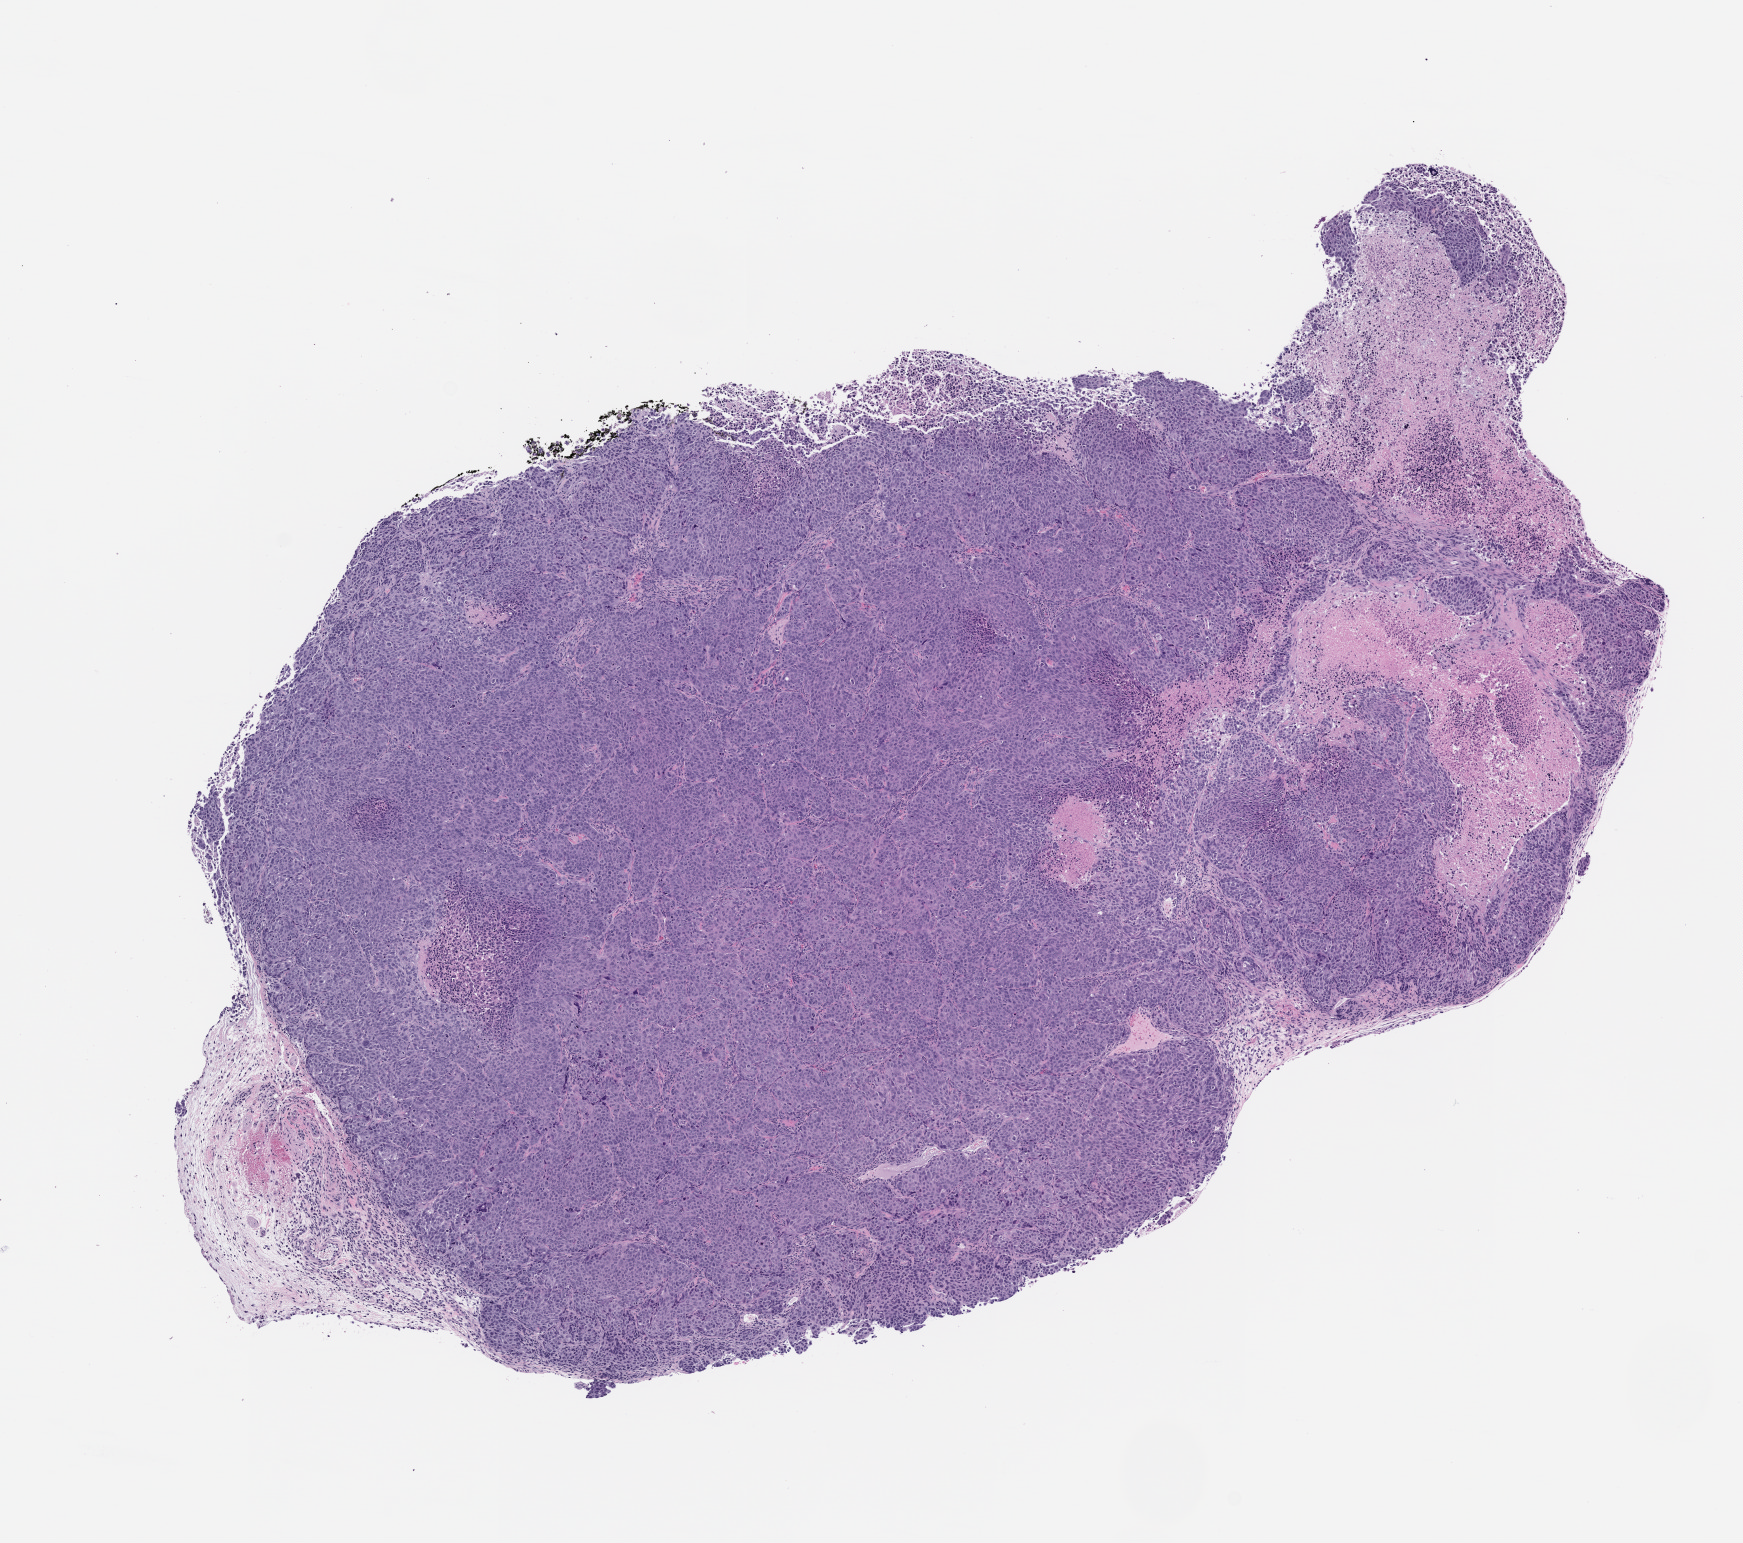
Hematoxylin and eosin (H&E) whole-slide image of a patient-derived xenograft (PDX) tumor grown in a mouse, passage 2, shown as a low-resolution overview of the whole scanned area (about 7.0 x 6.2 mm), FFPE section, originating tumor site category: lung.
- originating patient diagnosis: Lung Squamous Cell Carcinoma